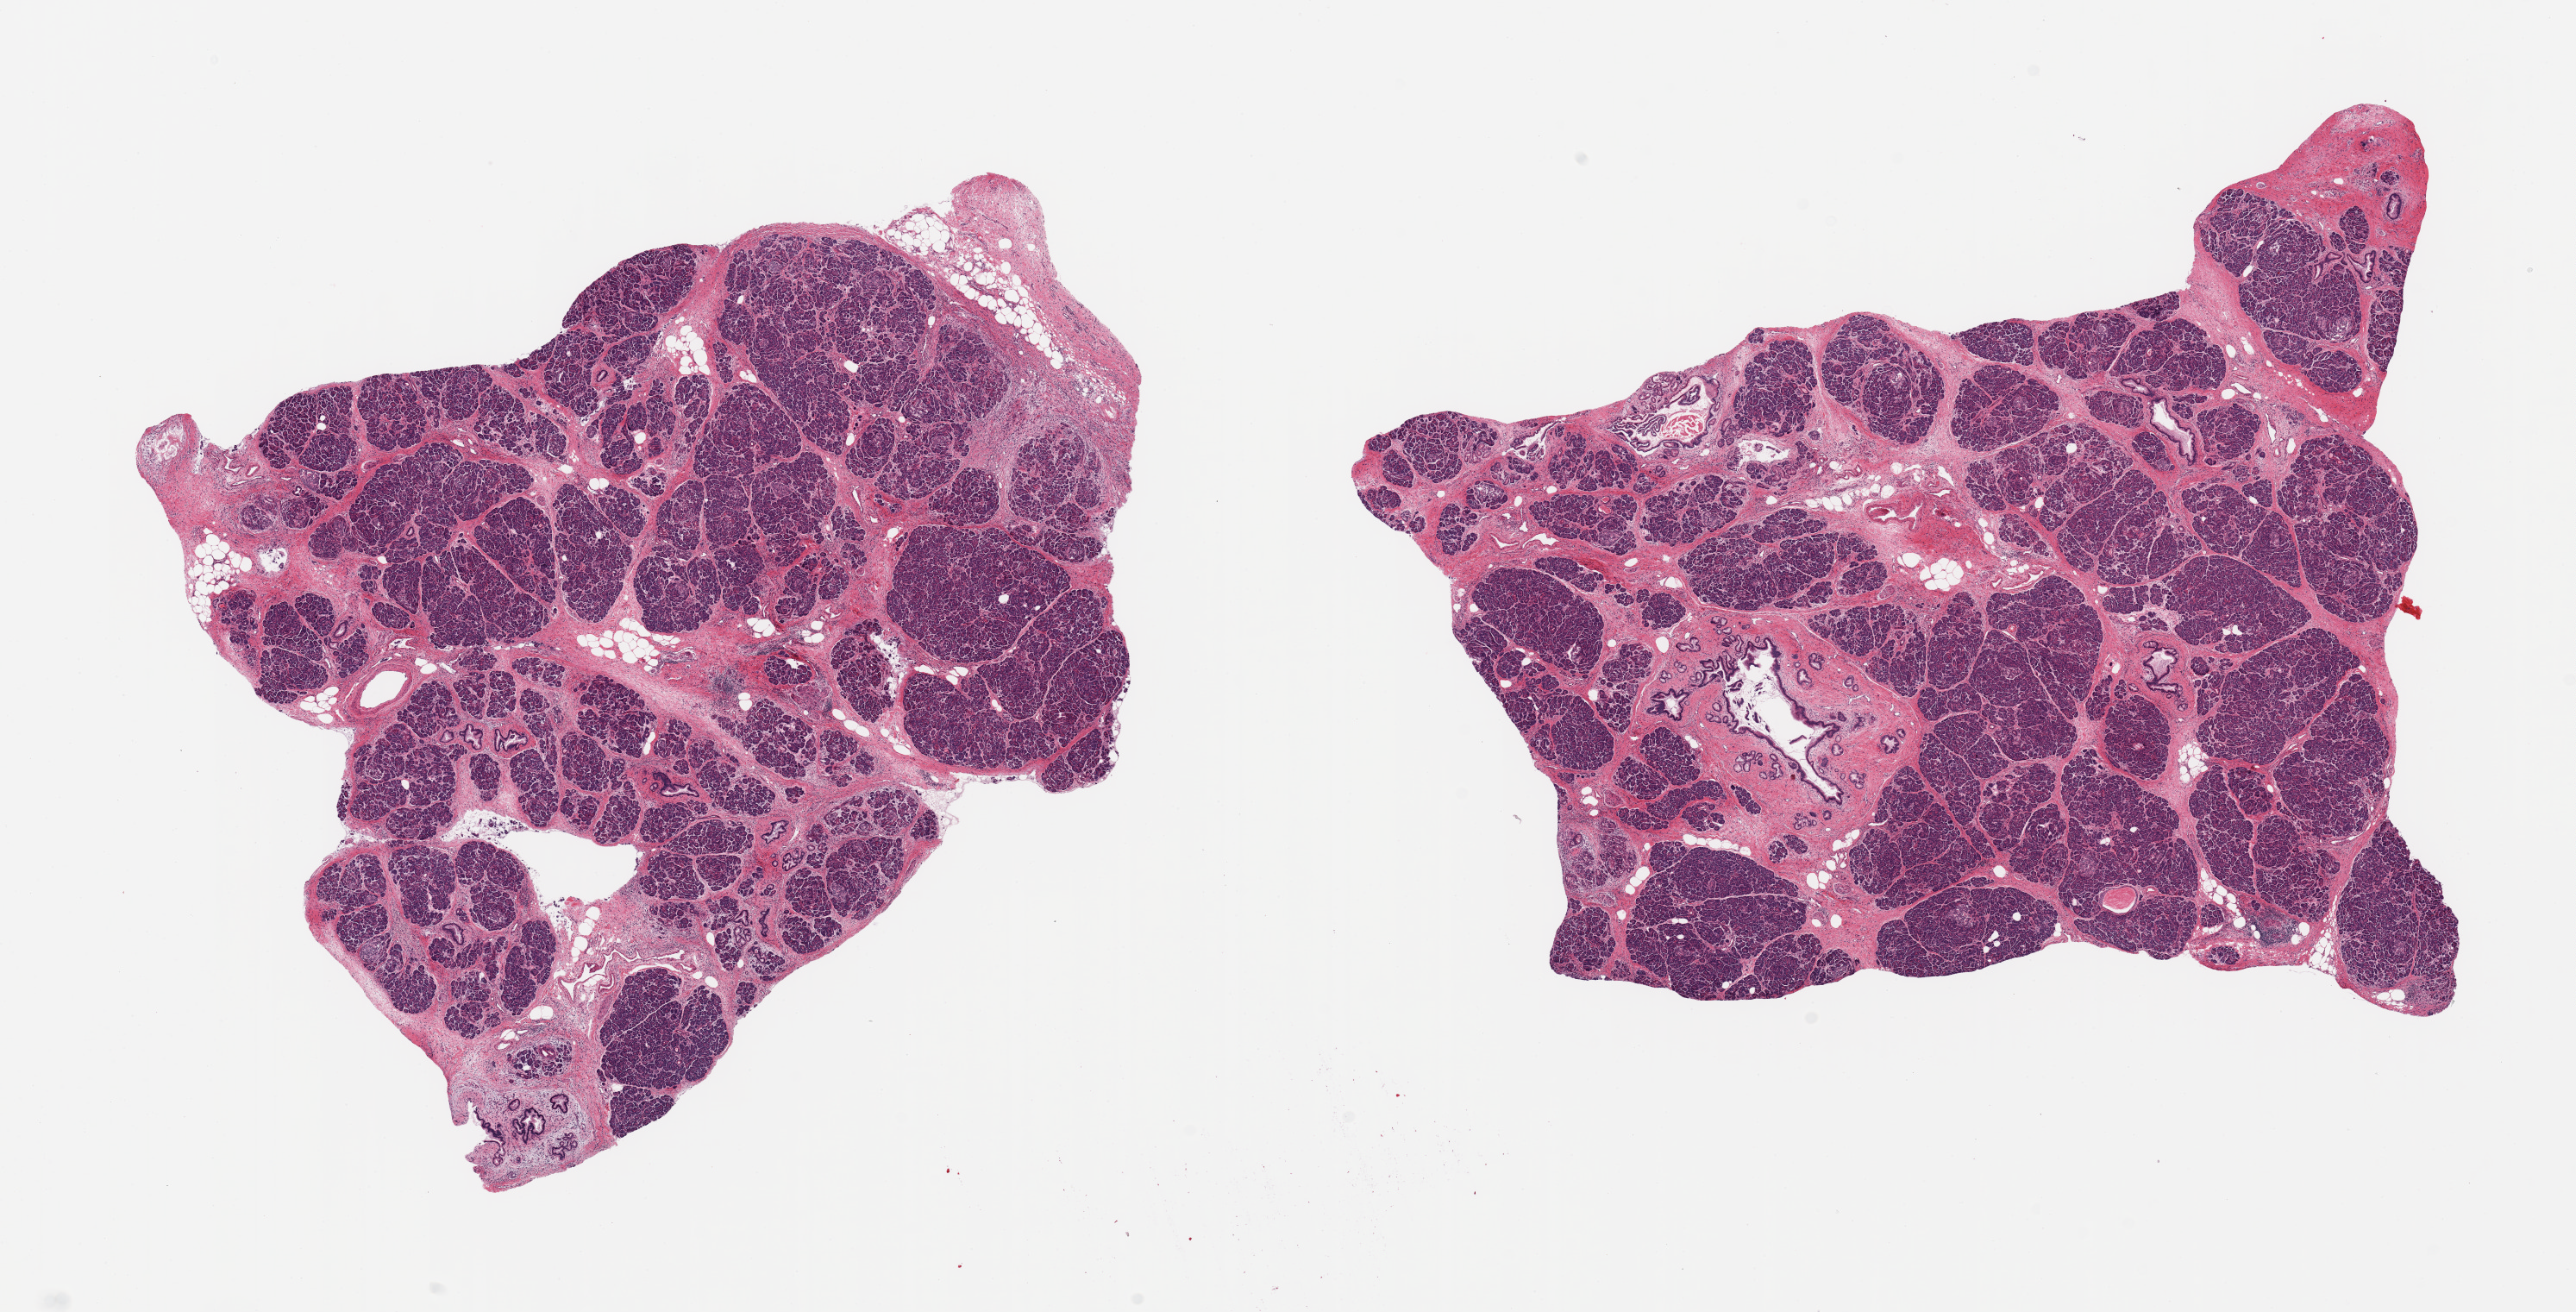
Digitized haematoxylin and eosin-stained section — a low-resolution overview of the entire scanned area, about 23.6 x 12.0 mm; PAXgene-fixed paraffin-embedded (PFPE) section; section of pancreas (target tissue); donor tissue sample. Female donor.
Pathologist's review note for this sample: 2 pieces; fibrosis.